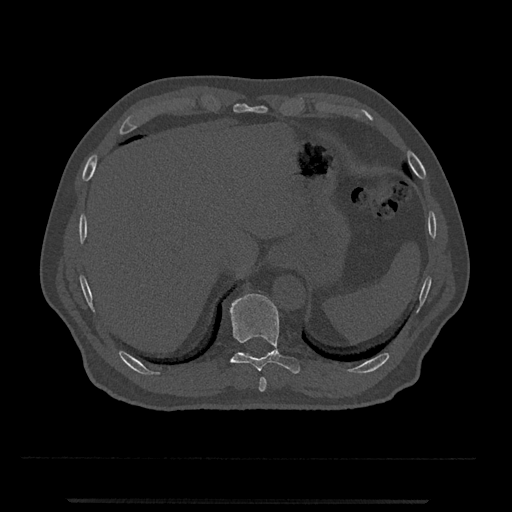
CT including the spine, one axial slice. Position 516 of 797 along the scan axis. Reconstruction kernel Br40s/3. 120 kVp. Bone window (W 1800 / L 400 HU). 512 × 512 image matrix. Patient: male, 63 years. From the clinical record (not read from this slice): primary cancer: prostate.
Structures marked on this image (semi-automatic segmentation, software-assisted and operator-edited):
- T10 vertebra: bounding box (x1, y1, x2, y2) in pixels: (229, 293, 300, 374)
- T9 vertebra: (259, 377, 267, 392)